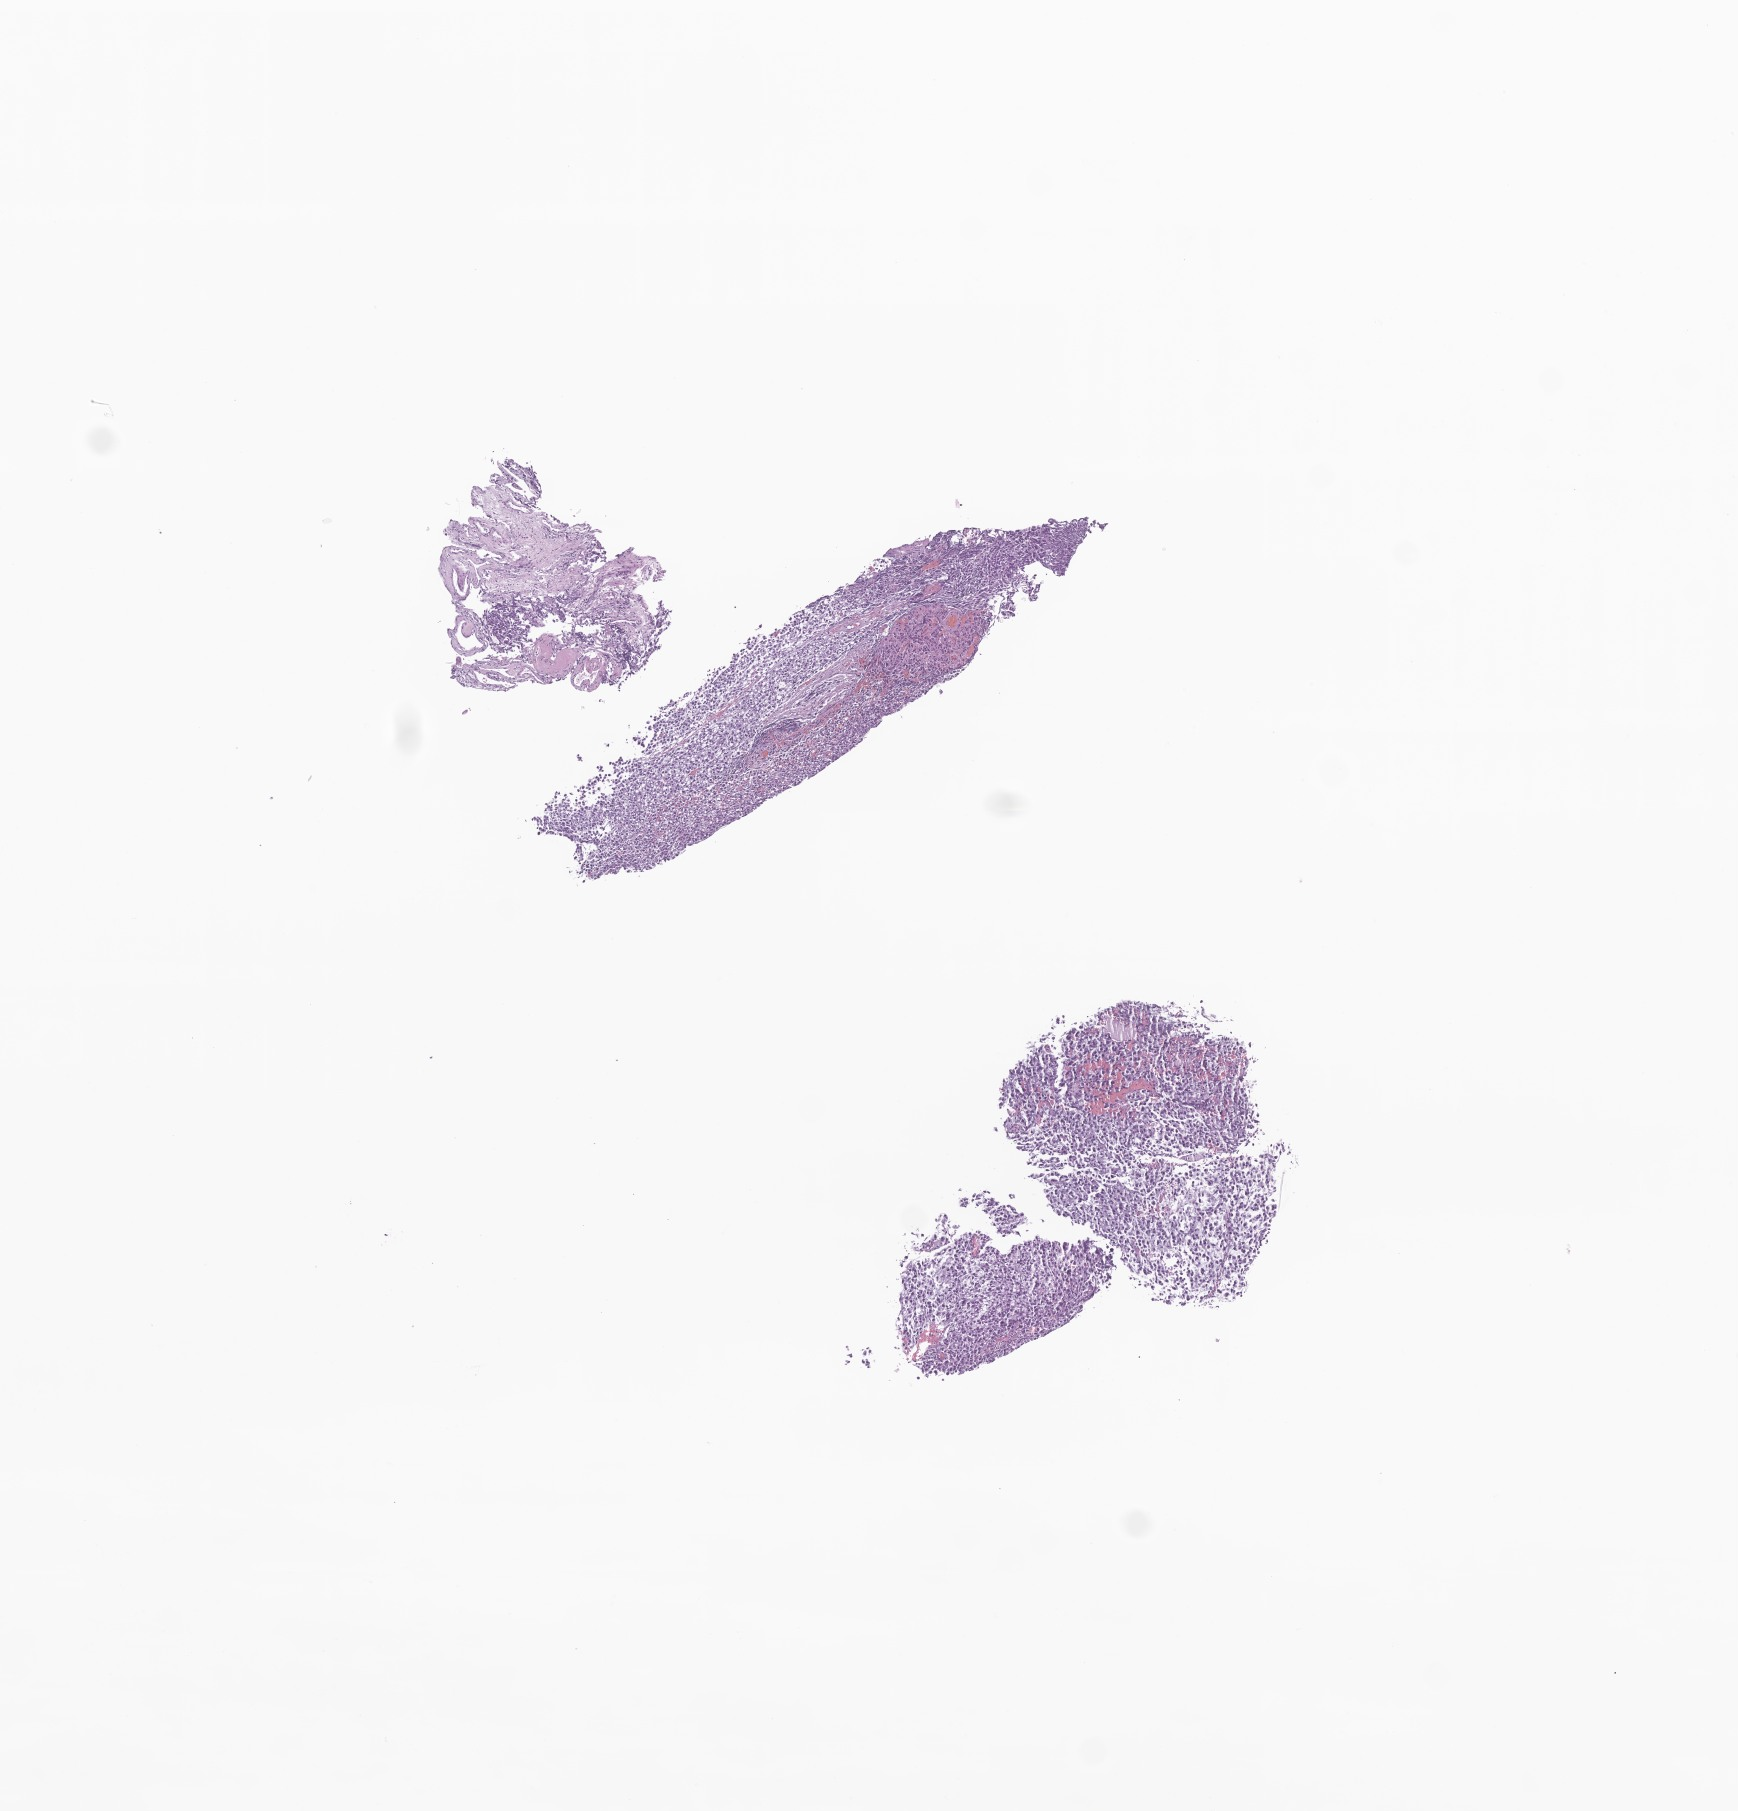
Digitized H&E-stained section of tumor tissue from the brain — low-resolution overview of the scanned area, about 7.3 x 7.6 mm; FFPE section. Male patient, age 212 months.
• diagnosis (ICD-O-3 morphology term): Germinoma